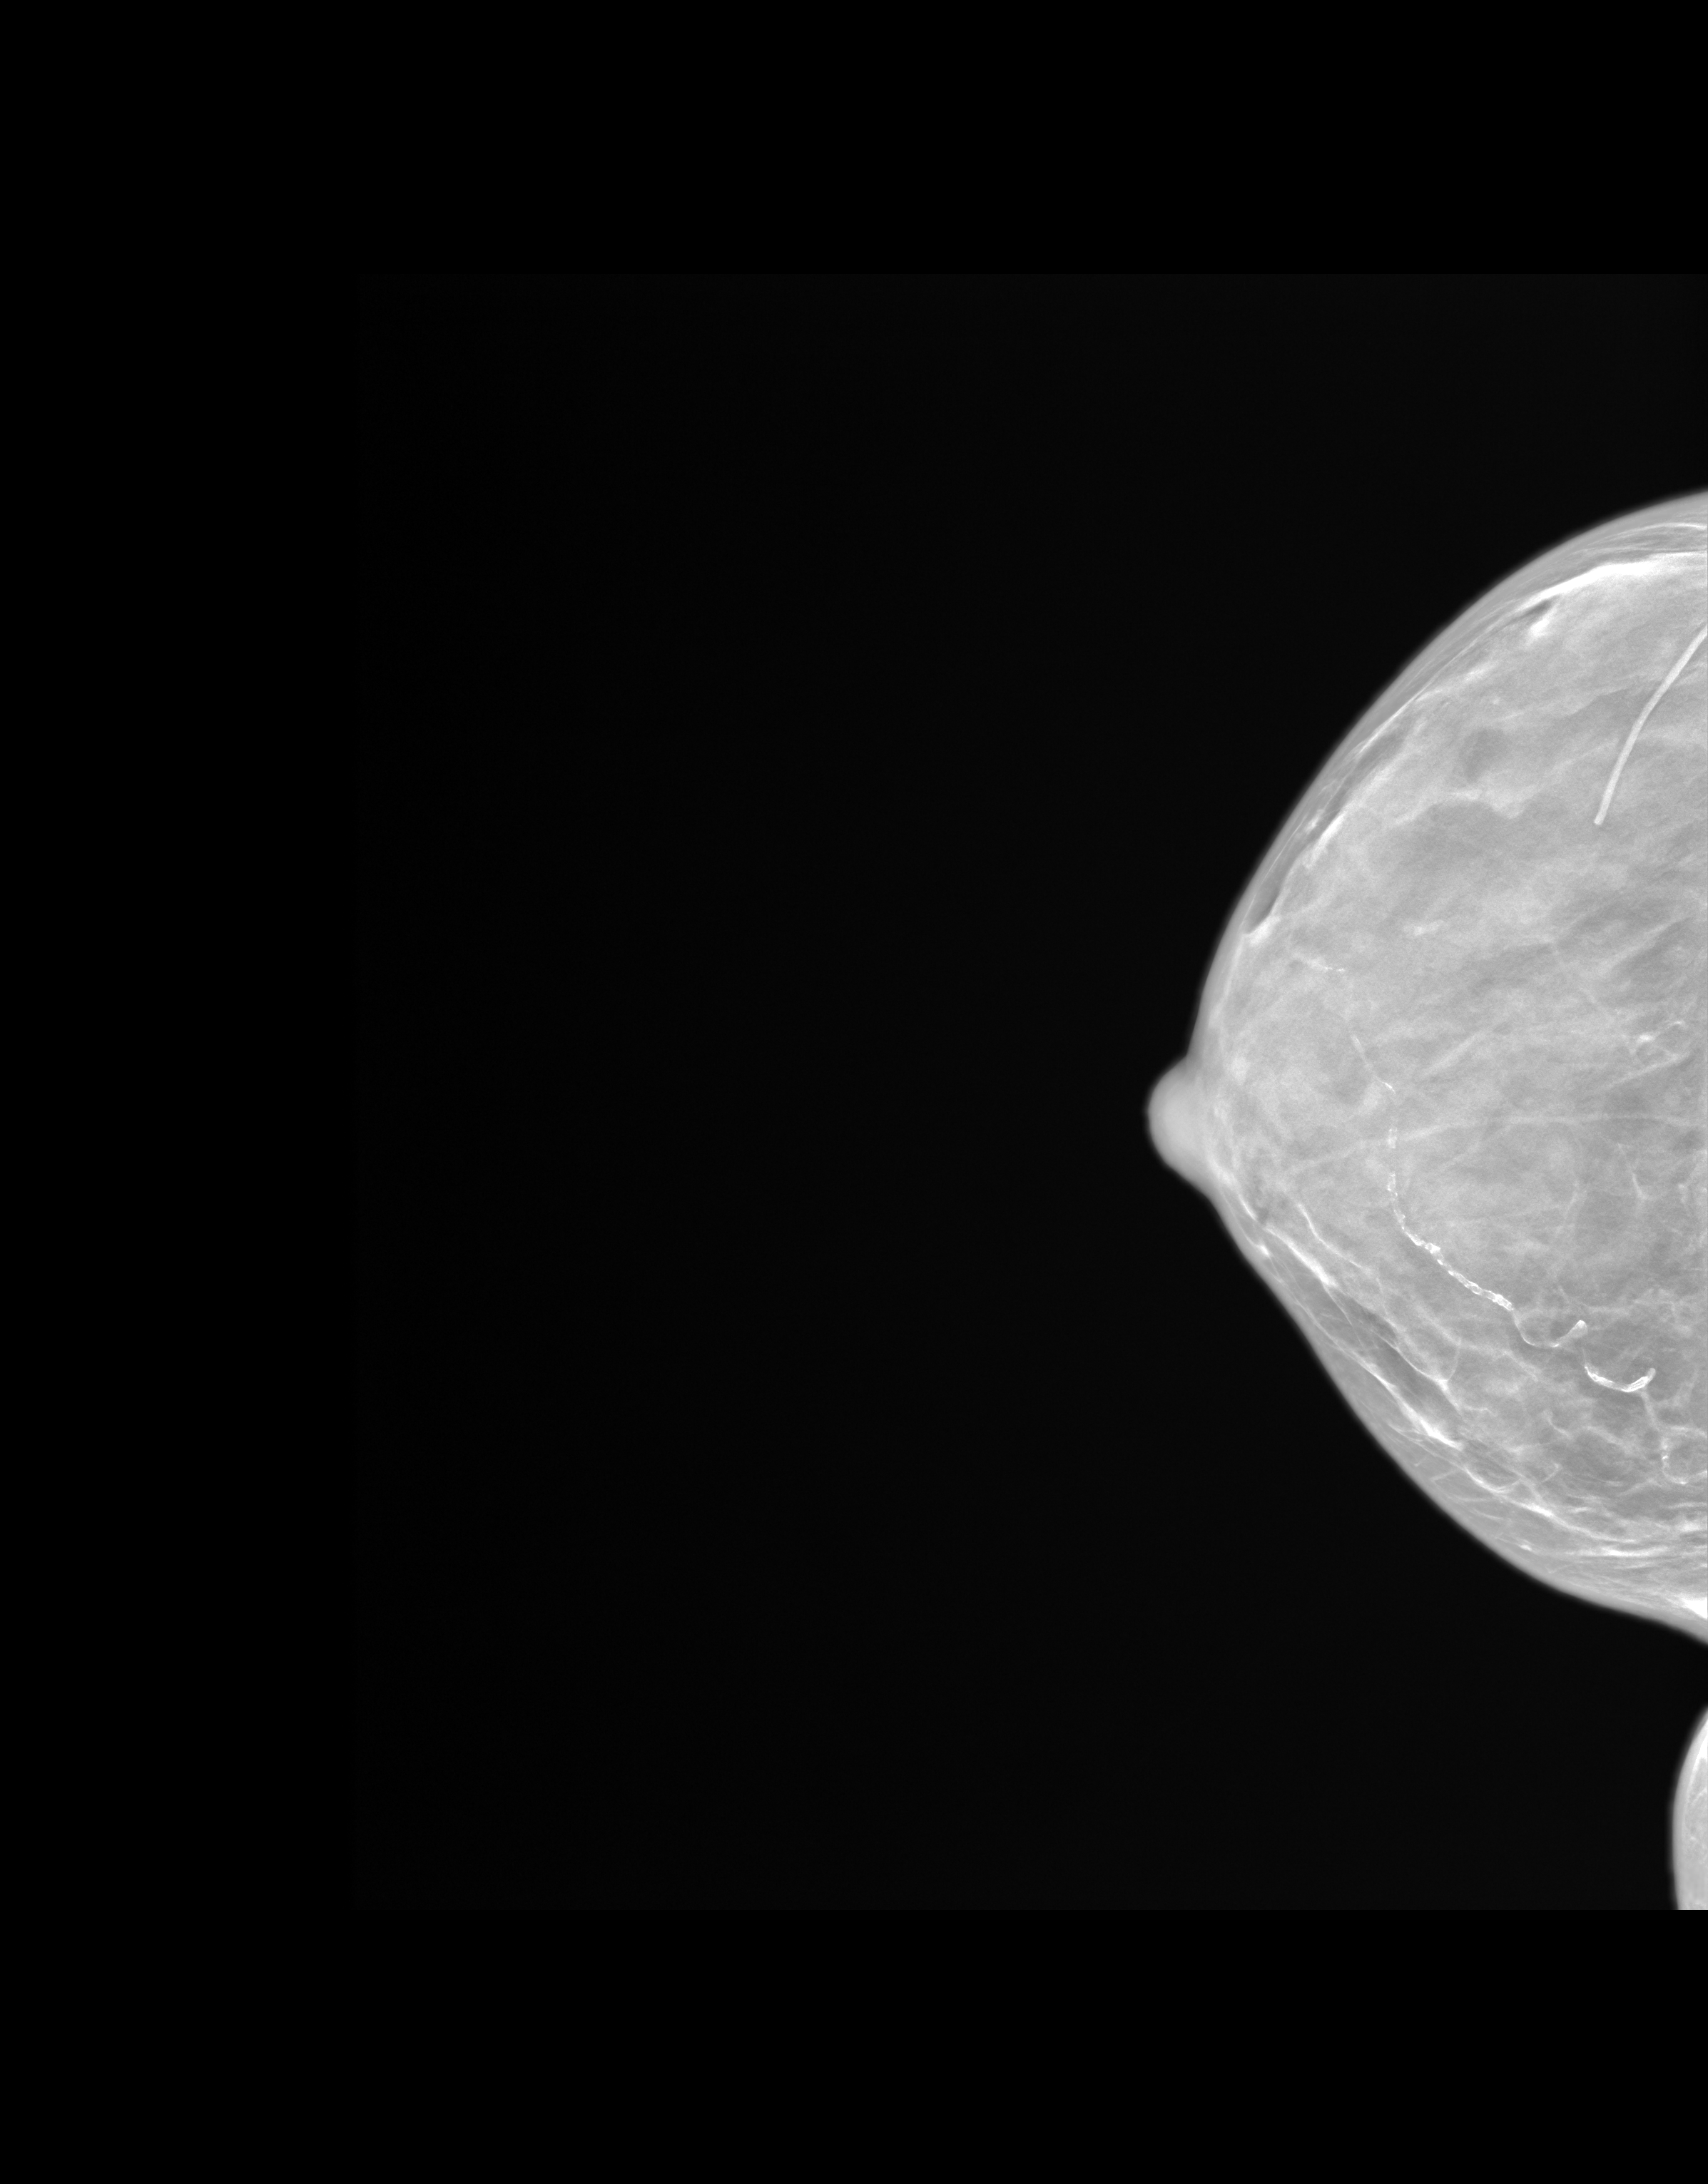
Synthetic 2-D view generated from a tomosynthesis acquisition (not an FFDM exposure), right breast, CC view, screening examination. Patient: female, 59 years.
Breast density at the screening exam (both breasts): extremely dense (BI-RADS density category d). Final BI-RADS category for the screening round (tomosynthesis exam, both breasts): category 1. Recall: no recall after this screen.